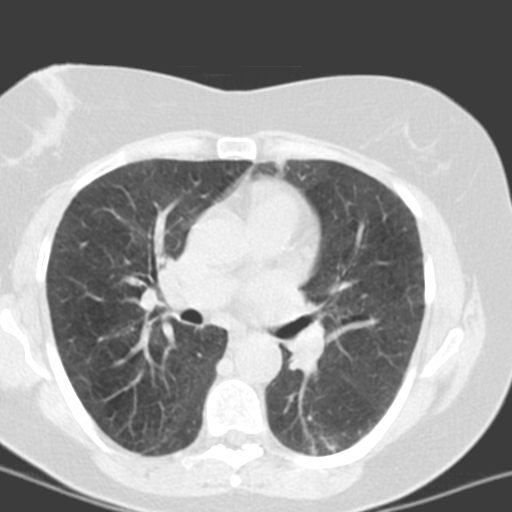
Low-dose screening chest CT, axial slice; third annual screen; lung window (W 1500 / L -600 HU); 512 × 512 image matrix, field of view 290 × 290 mm. Female, age 55 years at enrolment. Current smoker at enrolment.
Lesion marked by an expert reader, bounding box [x1, y1, x2, y2] px = [288, 413, 365, 464]. The screening reader recorded 6 non-calcified nodules or masses ≥4 mm on this exam (left lower lobe, left lower lobe, left upper lobe, lingula, lingula, right middle lobe); which of them this box marks is not recorded. Participant outcome: lung cancer diagnosed 357 days after this screen — adenocarcinoma with mixed subtypes, left lower lobe, poorly differentiated (G3), stage IA (AJCC 6th edition), 21 mm at pathology.